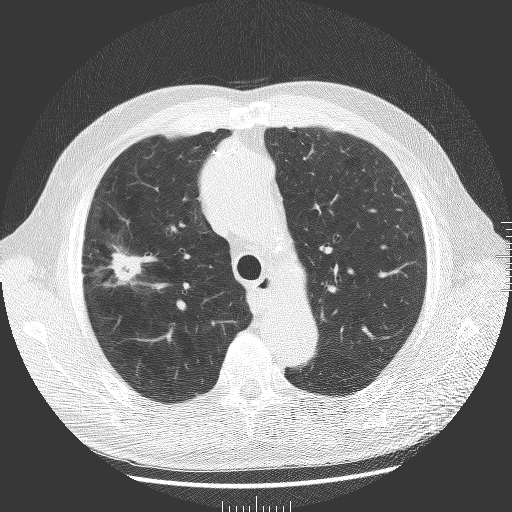
Low-dose screening chest CT, one axial slice. Slice 135 of 181 in the series (ordered by position). 120 kVp. Lung window (W 1500 / L -600 HU). 512 × 512 image matrix, field of view 380 × 380 mm.
Outlined on this slice (manually delineated by an expert):
- lesion 1 (tumor, upper lobe of right lung): bounding box (x1, y1, x2, y2) in pixels: (110, 251, 142, 285)